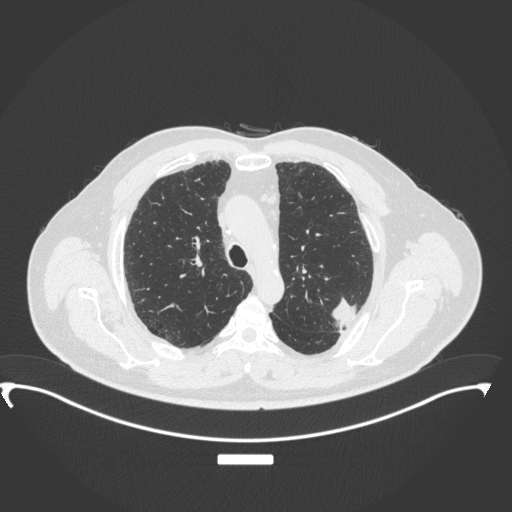
Chest CT, one axial slice; slice 260 of 350 in the series (ordered by position); 120 kVp; lung window (W 1500 / L -600 HU); 1 mm slice thickness; 512 × 512 image matrix, field of view 459 × 459 mm. Male patient, age 64 years. From the clinical record (not read from this slice): clinical TNM (as recorded): T1c N1 M1.
Outlined on this slice (rectangle marked by the reading radiologist):
- lung tumour (recorded histology: adenocarcinoma): bounding box [x1, y1, x2, y2] px = [327, 297, 362, 331]